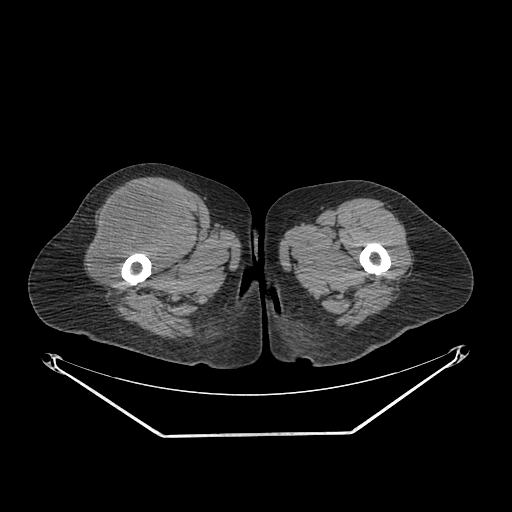
CT of an extremity soft-tissue mass (from a PET/CT study), one axial slice; position 265 of 311 along the scan axis; soft-tissue window (W 400 / L 40 HU); 3.75 mm slice thickness; 512 × 512 image matrix. Female patient. From the clinical record (not read from this slice): histological type: pleiomorphic undifferentiated sarcoma; grade: high; site of the primary tumour: right quadricep.
Annotated regions visible in this slice (expert contour drawn on MRI and transferred to this co-registered scan by the dataset authors):
- tumour plus oedema (research contour): box from (x=91, y=189) to (x=190, y=280) px
- tumour (research contour): (x=91, y=189)–(x=190, y=280)